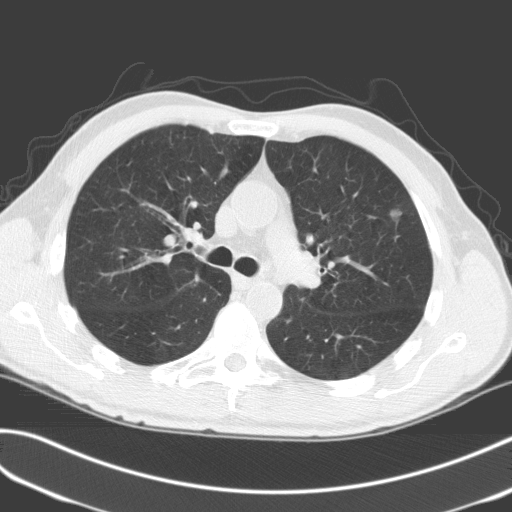
Low-dose screening chest CT, axial slice; third annual screen; lung window (W 1500 / L -600 HU); standard (soft-tissue) reconstruction kernel (C); slice 63 of 170 in the series; 512 × 512 image matrix, field of view 351 × 351 mm. Male, age 68 years at enrolment. Former smoker at enrolment.
- Expert reader's lesion annotation, bounding box <368,198,416,241> (left, top, right, bottom; pixels).
- Reader record for this screening exam (exam-level; its link to the box is not recorded): non-calcified nodule or mass ≥4 mm, left upper lobe, 9 × 7 mm, poorly defined margins, mixed attenuation, pre-existing on the prior screen: no.
- Official screen result: positive, other.
- Participant outcome: lung cancer diagnosed 364 days after this screen — adenocarcinoma, NOS, left upper lobe, moderately differentiated (G2), stage IA (AJCC 6th edition), 6 mm at pathology.